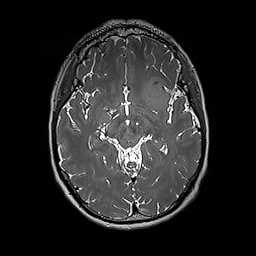
Brain MRI from a brain-tumour surgery series, one axial slice; slice 109 of 192 in the series (ordered by position); 256 × 256 image matrix, field of view 250 × 250 mm. From the clinical record (not read from this slice): histopathology: Glioblastoma; WHO grade: 4; IDH mutation: no.
Annotated regions visible in this slice (manually delineated by an expert):
- tumour: bounding box [x1, y1, x2, y2] px = [142, 76, 170, 110]